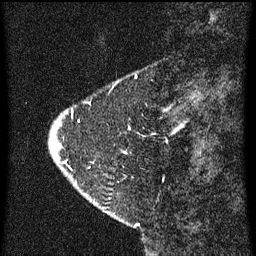
Breast MRI (dynamic contrast-enhanced), one sagittal slice; slice 13 of 60 in the series (ordered by position); dynamic contrast-enhanced series, image 2 of 3 at this slice position (ordered by acquisition); 1.5 T; TE 4.2 ms, TR 8 ms; 2 mm slice thickness; 256 × 256 image matrix, field of view 180 × 180 mm. Patient: female, 47 years.
Structures marked on this image (semi-automatic segmentation, software-assisted and operator-edited):
- analysis volume of interest (the breast-tissue region the enhancement analysis was run in; not a lesion): bounding box <50,104,169,199> (left, top, right, bottom; pixels)
- tumour enhancement mask (voxels above the 70 % enhancement threshold inside the analysis volume of interest): <72,116,127,153>